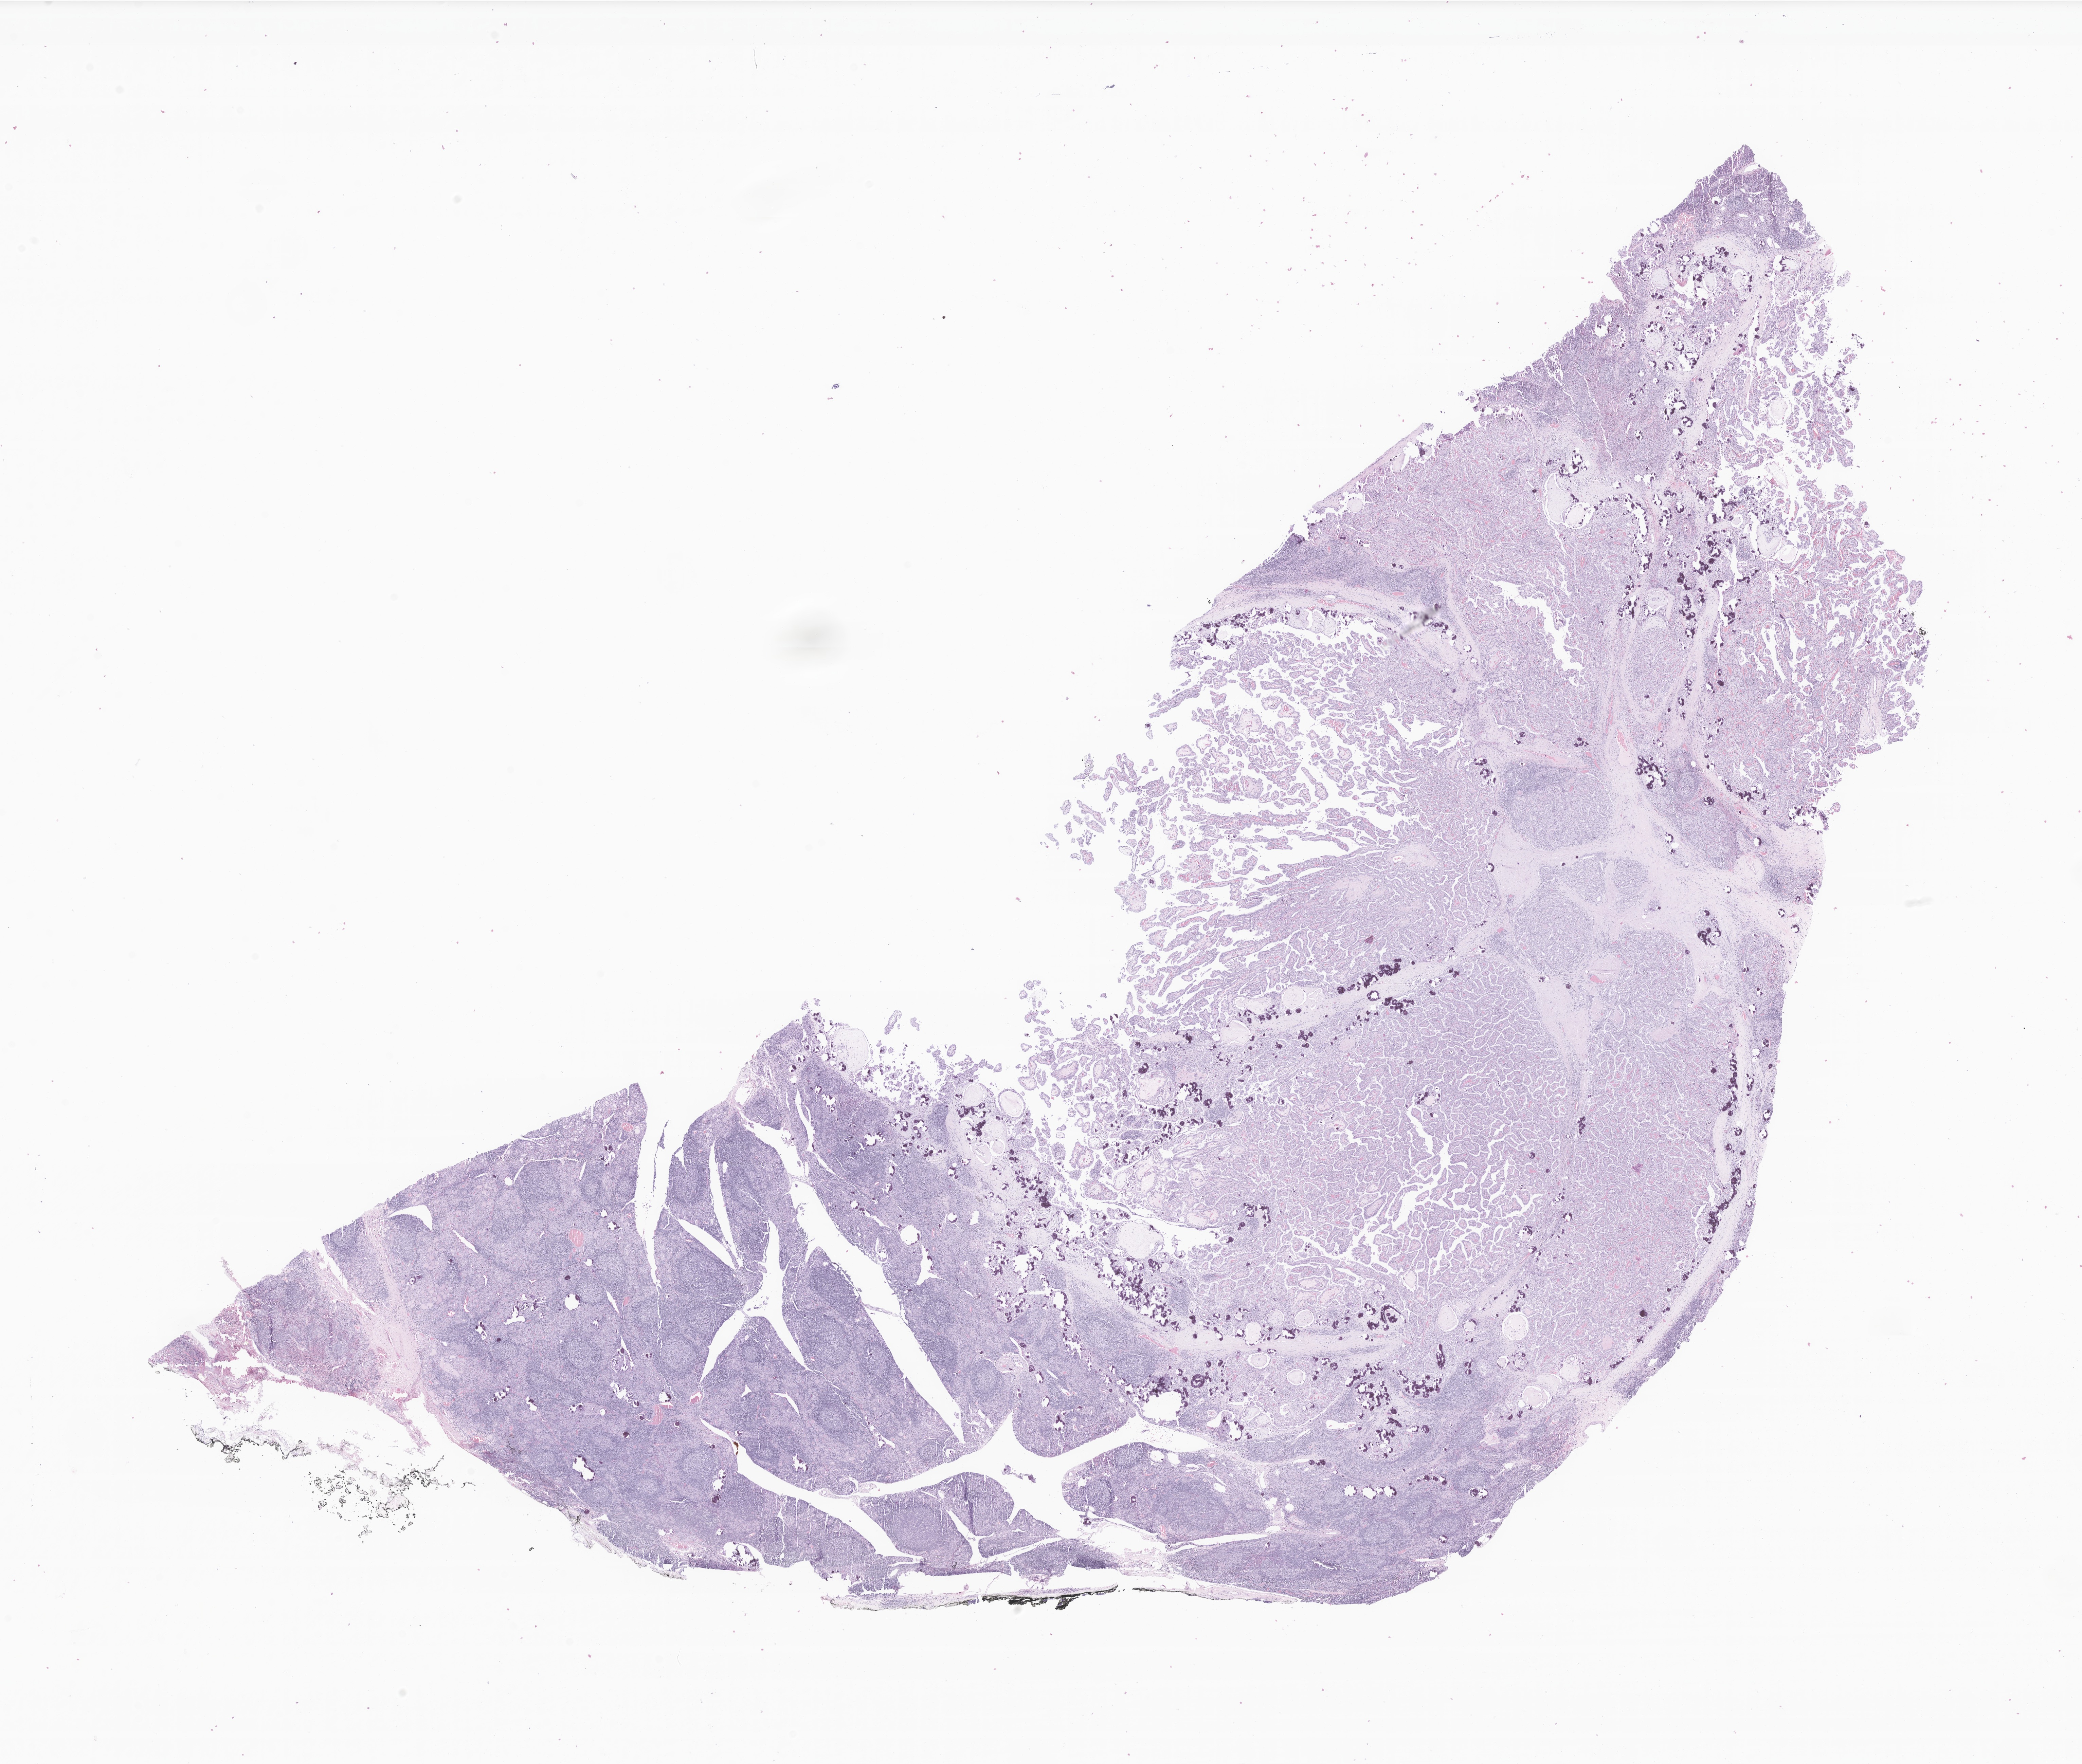
Whole-slide image, haematoxylin and eosin stain of tumor tissue from the thyroid — a low-resolution overview of the entire scanned area, about 25.8 x 21.9 mm. Formalin-fixed paraffin-embedded section. Patient: female, age 164 months (13 years 8 months).
- diagnosis: Papillary carcinoma, NOS